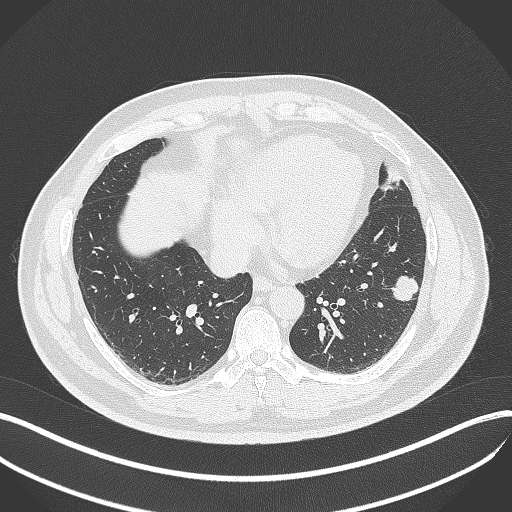
Chest CT, one axial slice. Position 148 of 429 along the scan axis. Reconstruction kernel B70f. 120 kVp. Lung window (W 1500 / L -600 HU). 1 mm slice thickness. 512 × 512 image matrix, field of view 400 × 400 mm. Patient: male, 39 years. Case-level facts recorded for this patient, not image findings: clinical TNM (as recorded): T2a N0 M0; histopathological grade: G2-3.
Annotated regions visible in this slice (rectangle marked by the reading radiologist):
- lung tumour (recorded histology: adenocarcinoma): bounding box [x1, y1, x2, y2] px = [387, 273, 423, 306]